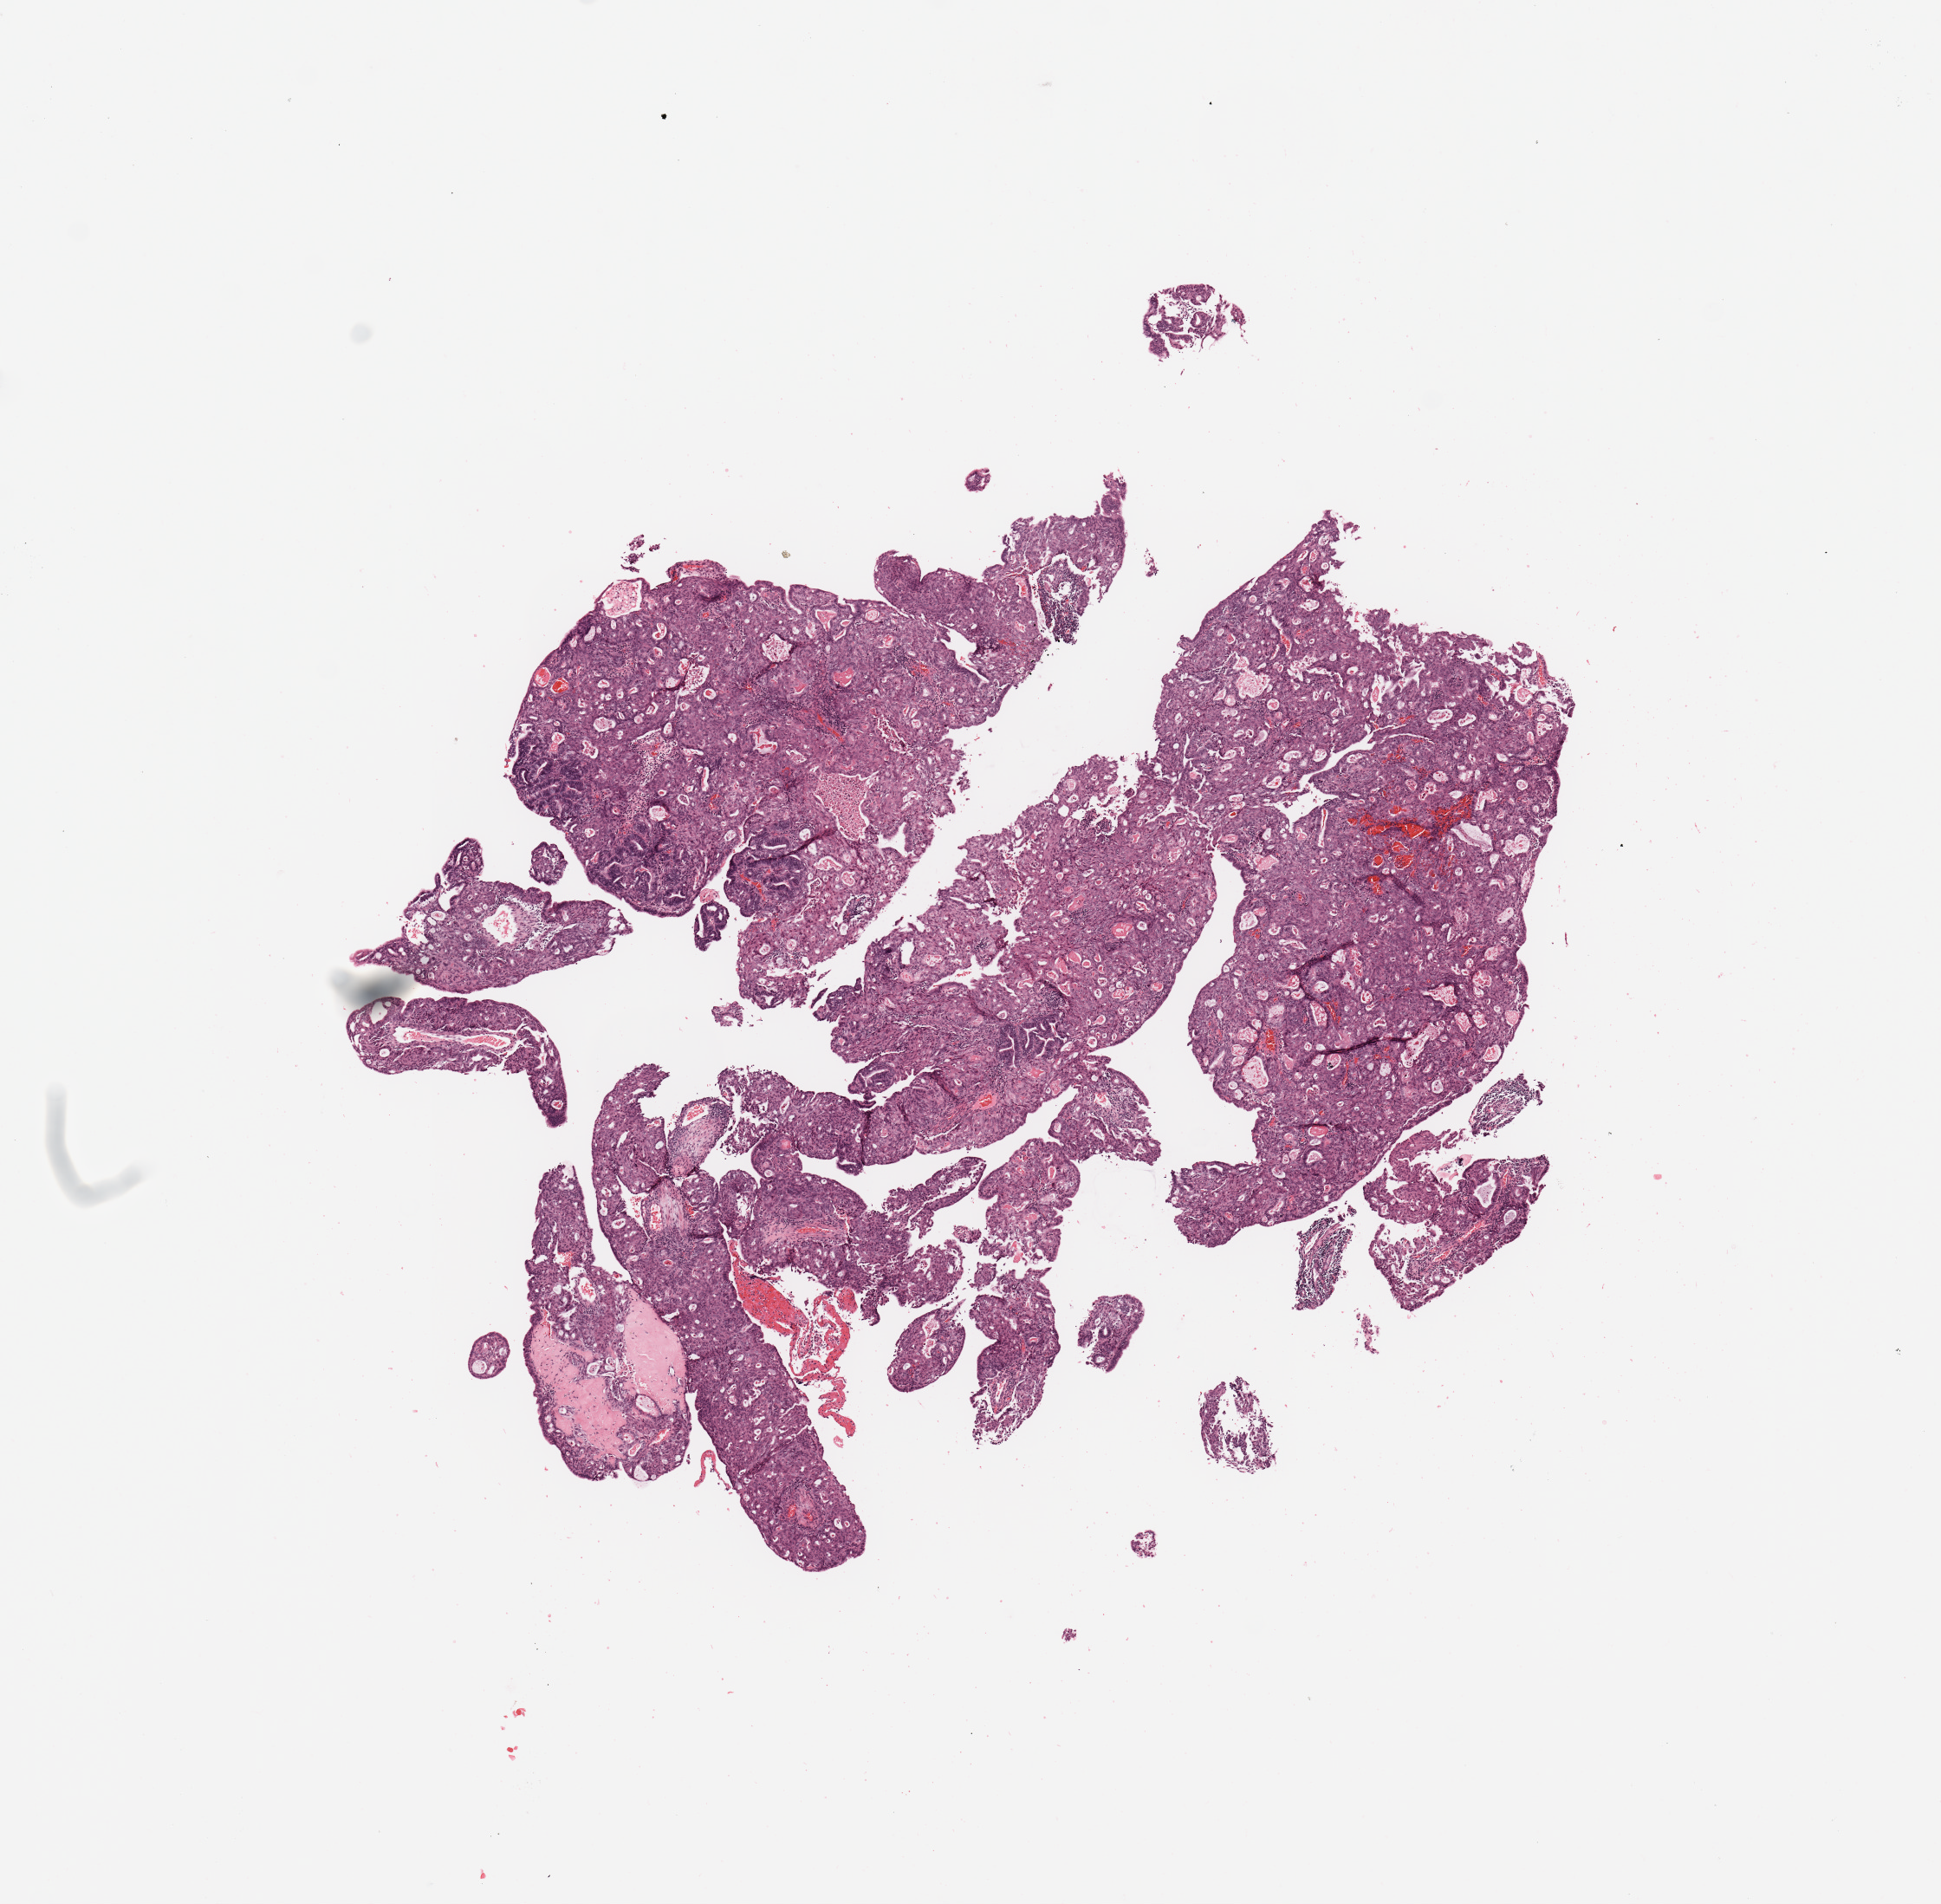
Hematoxylin and eosin (H&E) stained whole-slide image — whole scanned area (about 8.9 x 8.7 mm, from a 20x scan) shown as a low-resolution overview. Uterus, tumour tissue. 60-year-old female patient. Histologic grade: G1 (well differentiated).
Diagnosis: Endometrioid adenocarcinoma, NOS. AJCC pathologic stage: I.